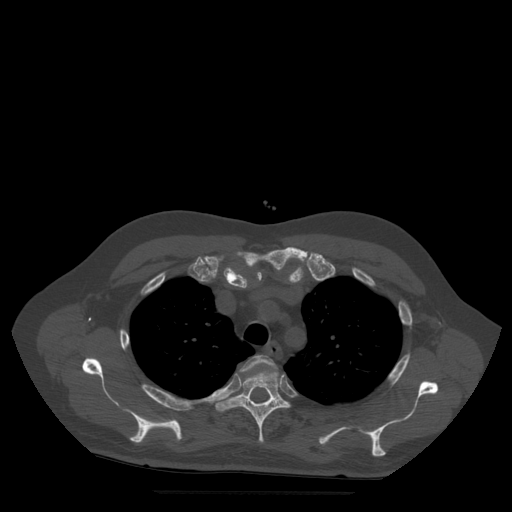
CT including the spine, one axial slice; bone window (W 1800 / L 400 HU); 512 × 512 image matrix, field of view 420 × 420 mm. Patient age 72 years. Case-level facts recorded for this patient, not image findings: primary cancer: prostate.
Annotated regions visible in this slice (semi-automatically segmented with operator editing):
- T3 vertebra: box from (x=240, y=355) to (x=278, y=372) px
- T4 vertebra: (x=216, y=370)–(x=291, y=443)